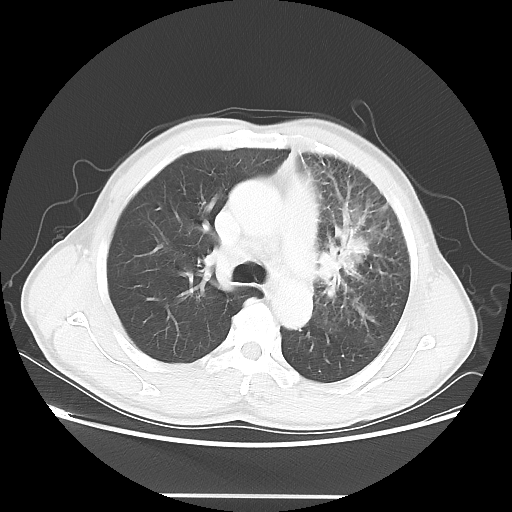
Chest CT, one axial slice. Slice 35 of 55 in the series (ordered by position). Reconstruction kernel LUNG. 100 kVp. Lung window (W 1500 / L -600 HU). 512 × 512 image matrix, field of view 398 × 398 mm. Patient: male, 60 years. From the clinical record (not read from this slice): clinical TNM (as recorded): T3 N3 M0.
Structures marked on this image (bounding box drawn by a radiologist):
- lung tumour (recorded histology: adenocarcinoma): box from (x=334, y=202) to (x=374, y=268) px